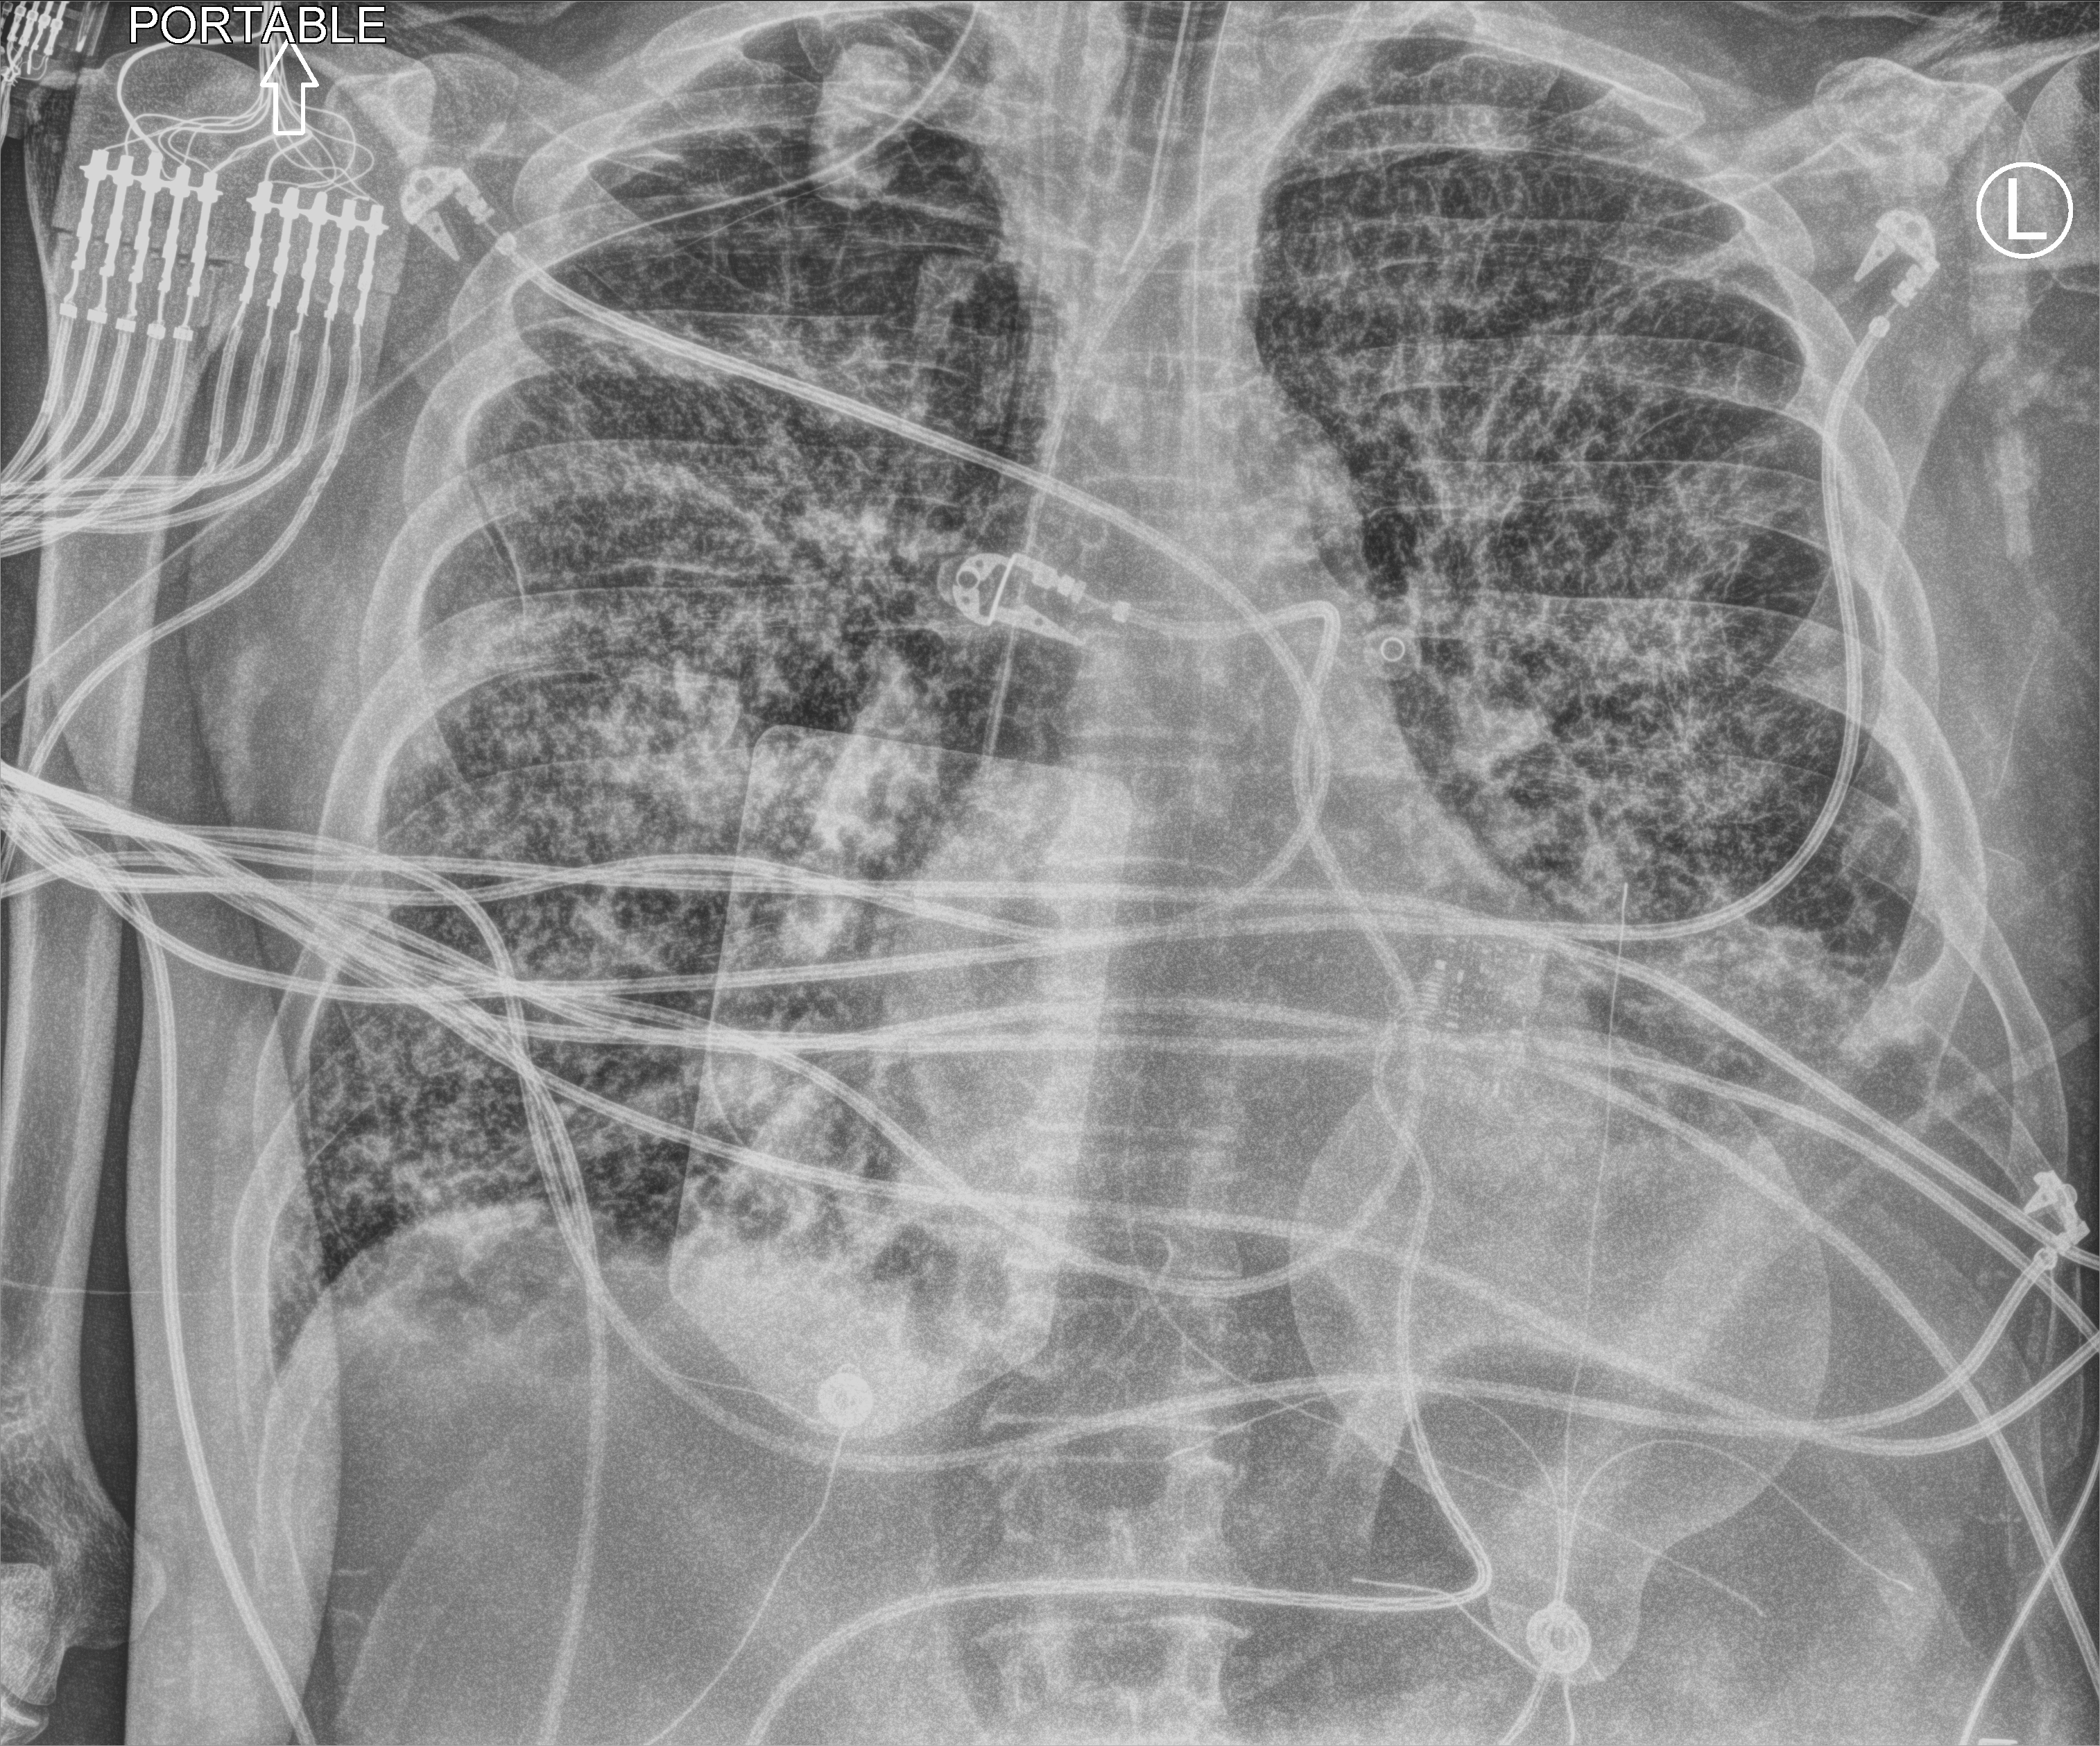
Bedside chest radiograph (computed radiography), anteroposterior (AP) projection. Male patient hospitalised with COVID-19, age 75–90 years.
From the hospital-stay record, not from the radiograph (when in the stay this image was taken is not recorded): admitted to intensive care during this hospital stay: yes; mechanically ventilated during this hospital stay: yes; other chronic lung disease (admission record): yes.